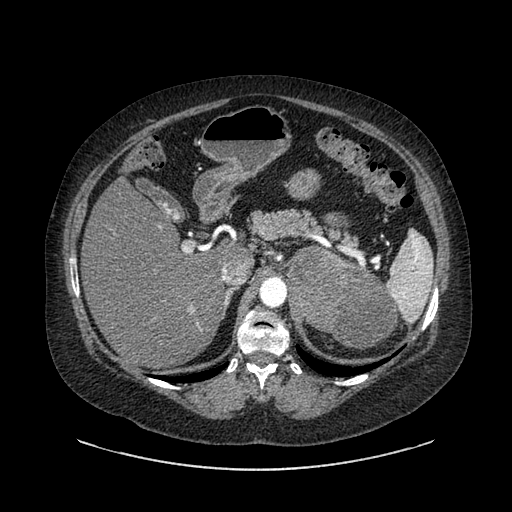
Contrast-enhanced abdominal CT, one axial slice. Slice 594 of 769 in the series (ordered by position). 120 kVp. Intravenous contrast given. Soft-tissue window (W 400 / L 40 HU). 0.62 mm slice thickness. 512 × 512 image matrix, field of view 460 × 460 mm. Female patient, age 61 years. Case-level facts recorded for this patient, not image findings: diagnosis: adrenocortical carcinoma; tumour side: left adrenal; tumour size at pathology: 13 cm; Ki-67 index: 79 %; stage (as recorded): 2.
Outlined on this slice (semi-automatically segmented with operator editing):
- mass: bounding box <289,250,396,348> (left, top, right, bottom; pixels)